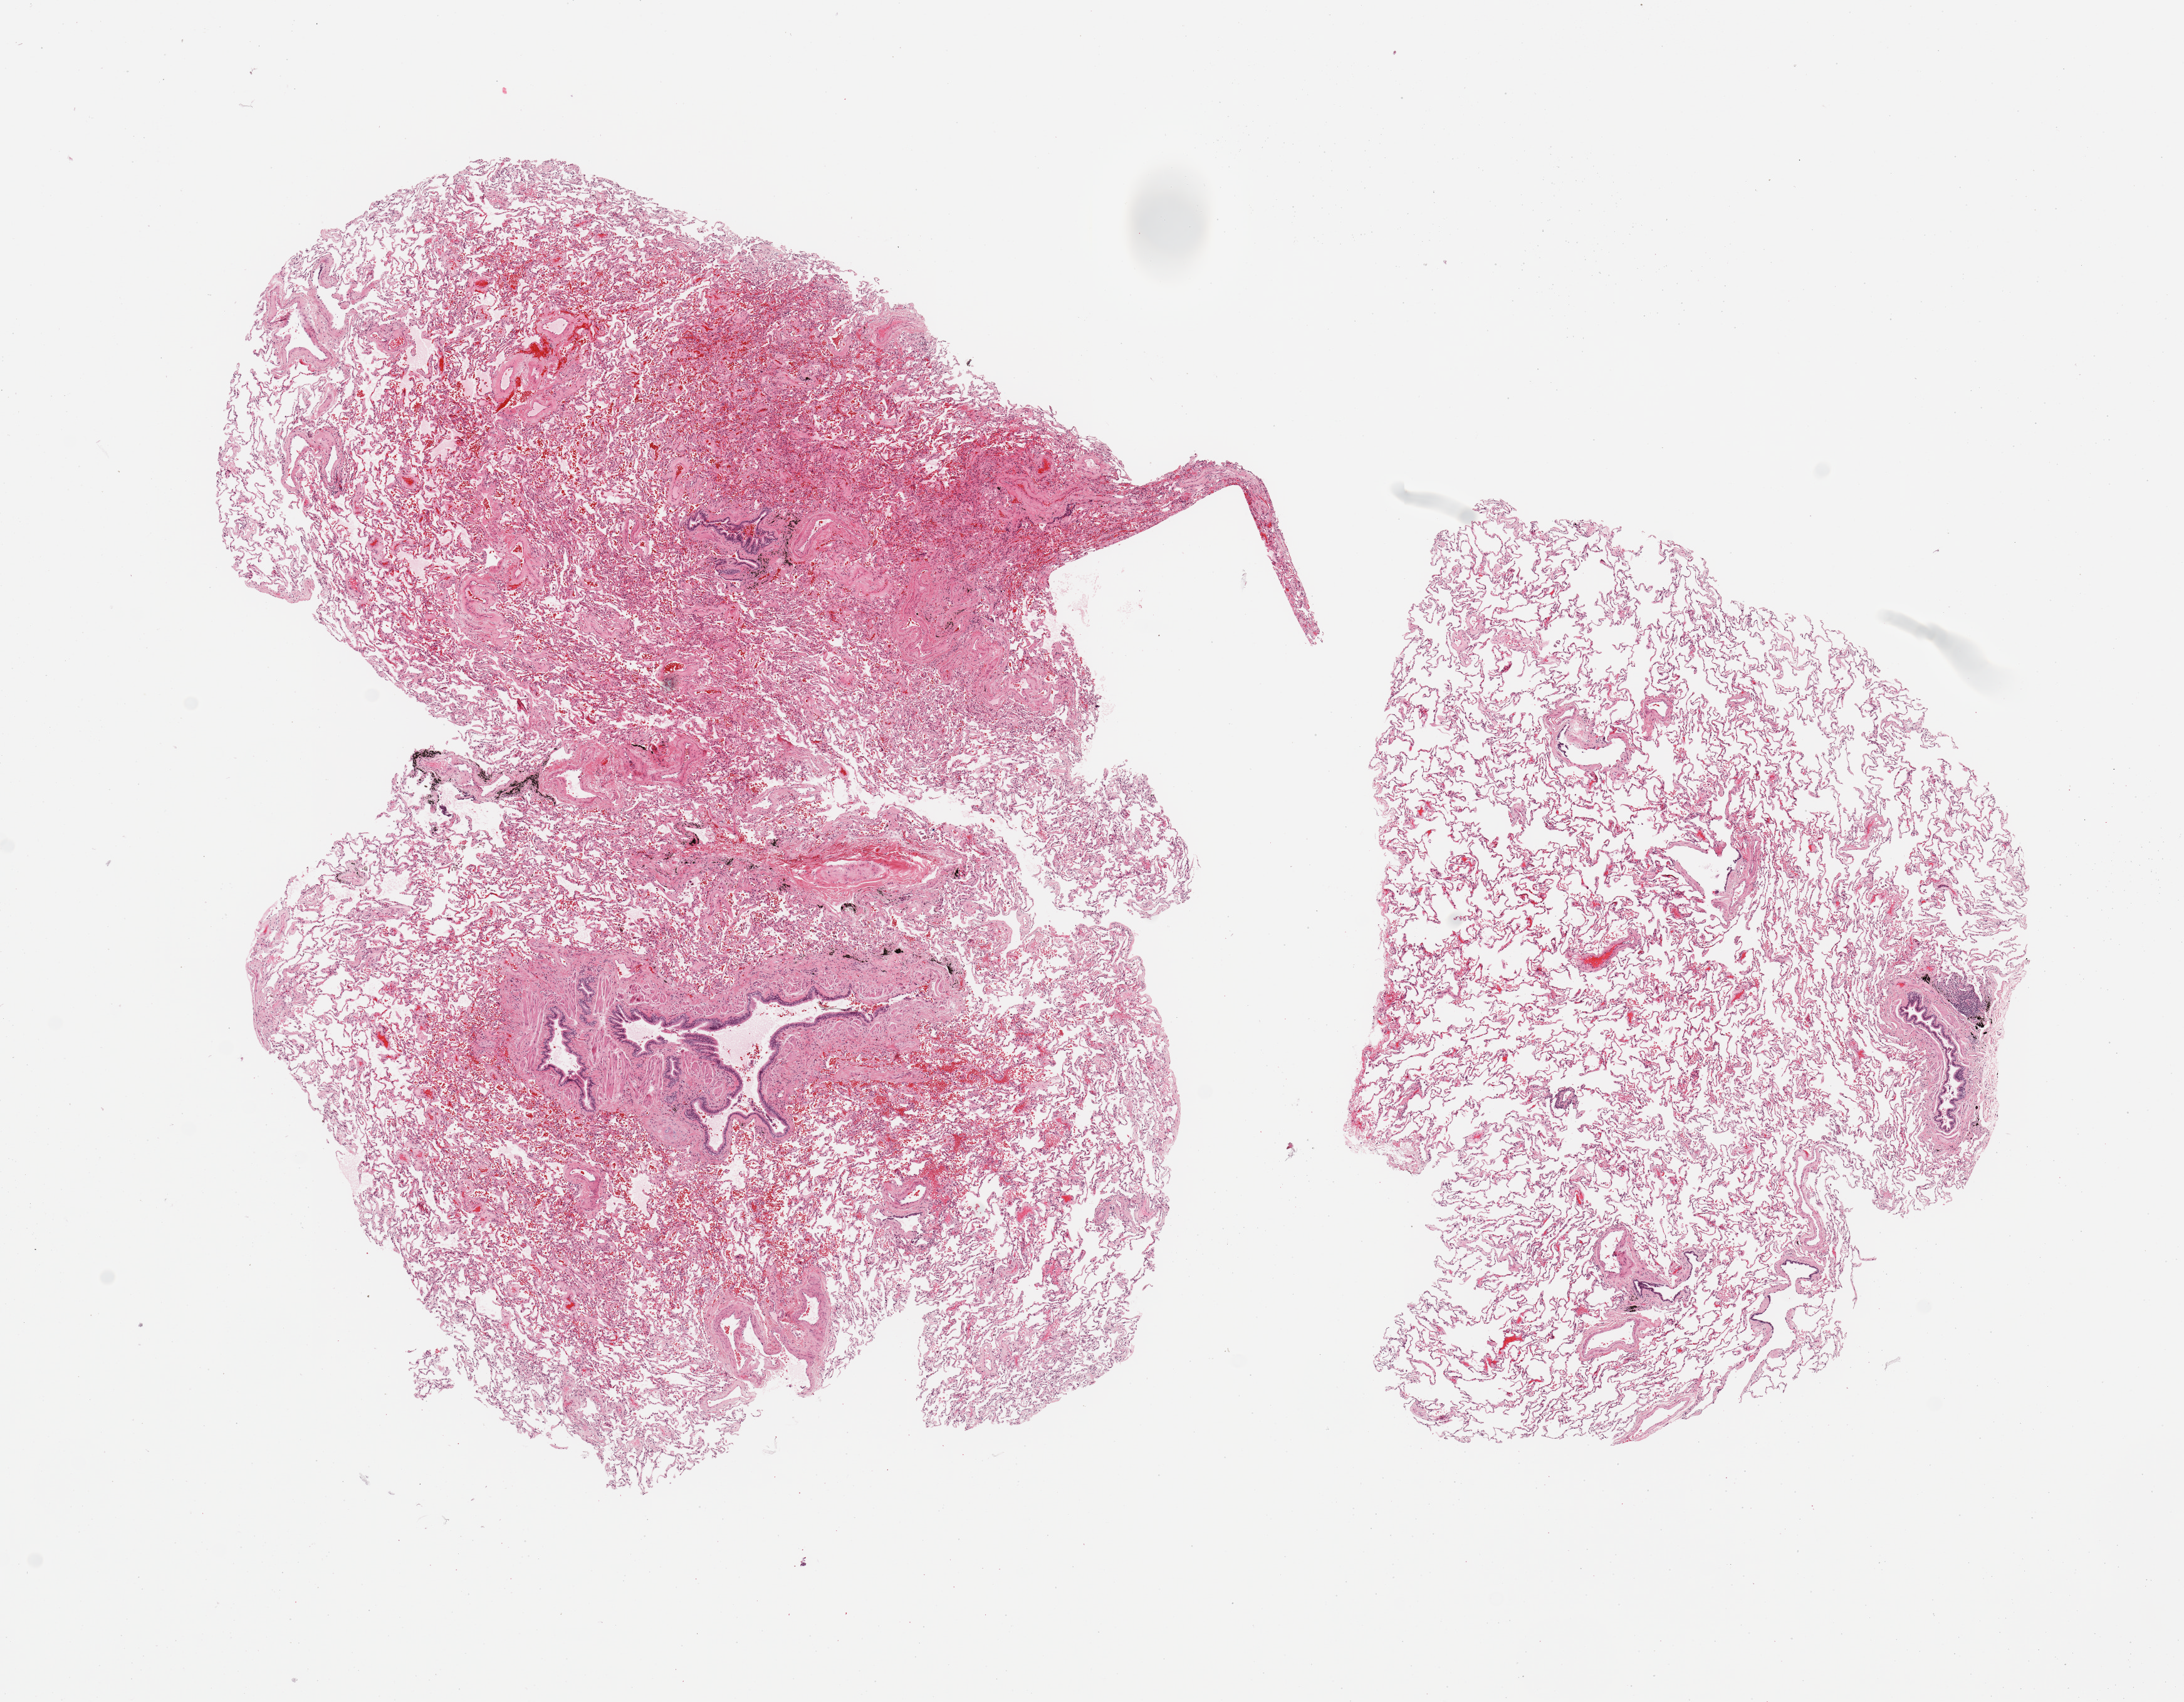
Hematoxylin and eosin (H&E) stained whole-slide image, shown as a low-resolution overview of the whole scanned area (about 13.8 x 10.7 mm, slide scanned at 20x). Normal (non-tumour) tissue sample, sampled site: lung. 74-year-old male patient.
* this section: normal (non-tumour) tissue from the same patient
* patient diagnosis: Adenocarcinoma, NOS